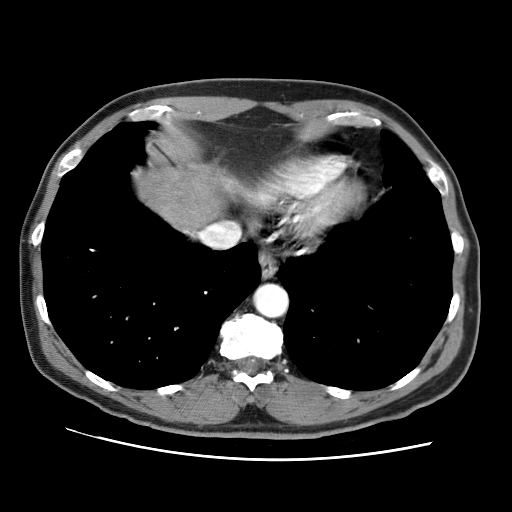
Contrast-enhanced abdominal CT (liver protocol), one axial slice. Position 66 of 71 along the scan axis. Reconstruction kernel STANDARD. 120 kVp. Soft-tissue window (W 400 / L 40 HU). 512 × 512 image matrix. Case-level facts recorded for this patient, not image findings: diagnosis: hepatocellular carcinoma (patient treated with transarterial chemoembolisation; whether this scan precedes or follows treatment is not stated here); TNM stage (as recorded): Stage-II; Child-Pugh class: A; tumour differentiation: well differentiated; tumour size: 4.6 cm.
Structures marked on this image (semi-automatically segmented with operator editing):
- liver parenchyma outside the tumour (the mass and vessels are separate outlines, so this box may not span the whole liver): box from (x=136, y=164) to (x=220, y=224) px